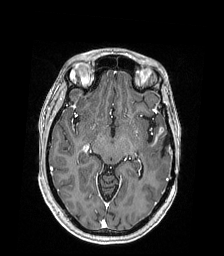
Brain MRI from a brain-tumour surgery series, one axial slice. Position 110 of 168 along the scan axis. T1-weighted post-contrast. 224 × 256 image matrix, field of view 224 × 256 mm. Case-level facts recorded for this patient, not image findings: histopathology: Astrocytoma; WHO grade: 4; IDH mutation: yes.
Structures marked on this image (manually delineated by an expert):
- tumour: bounding box [x1, y1, x2, y2] px = [153, 124, 166, 145]